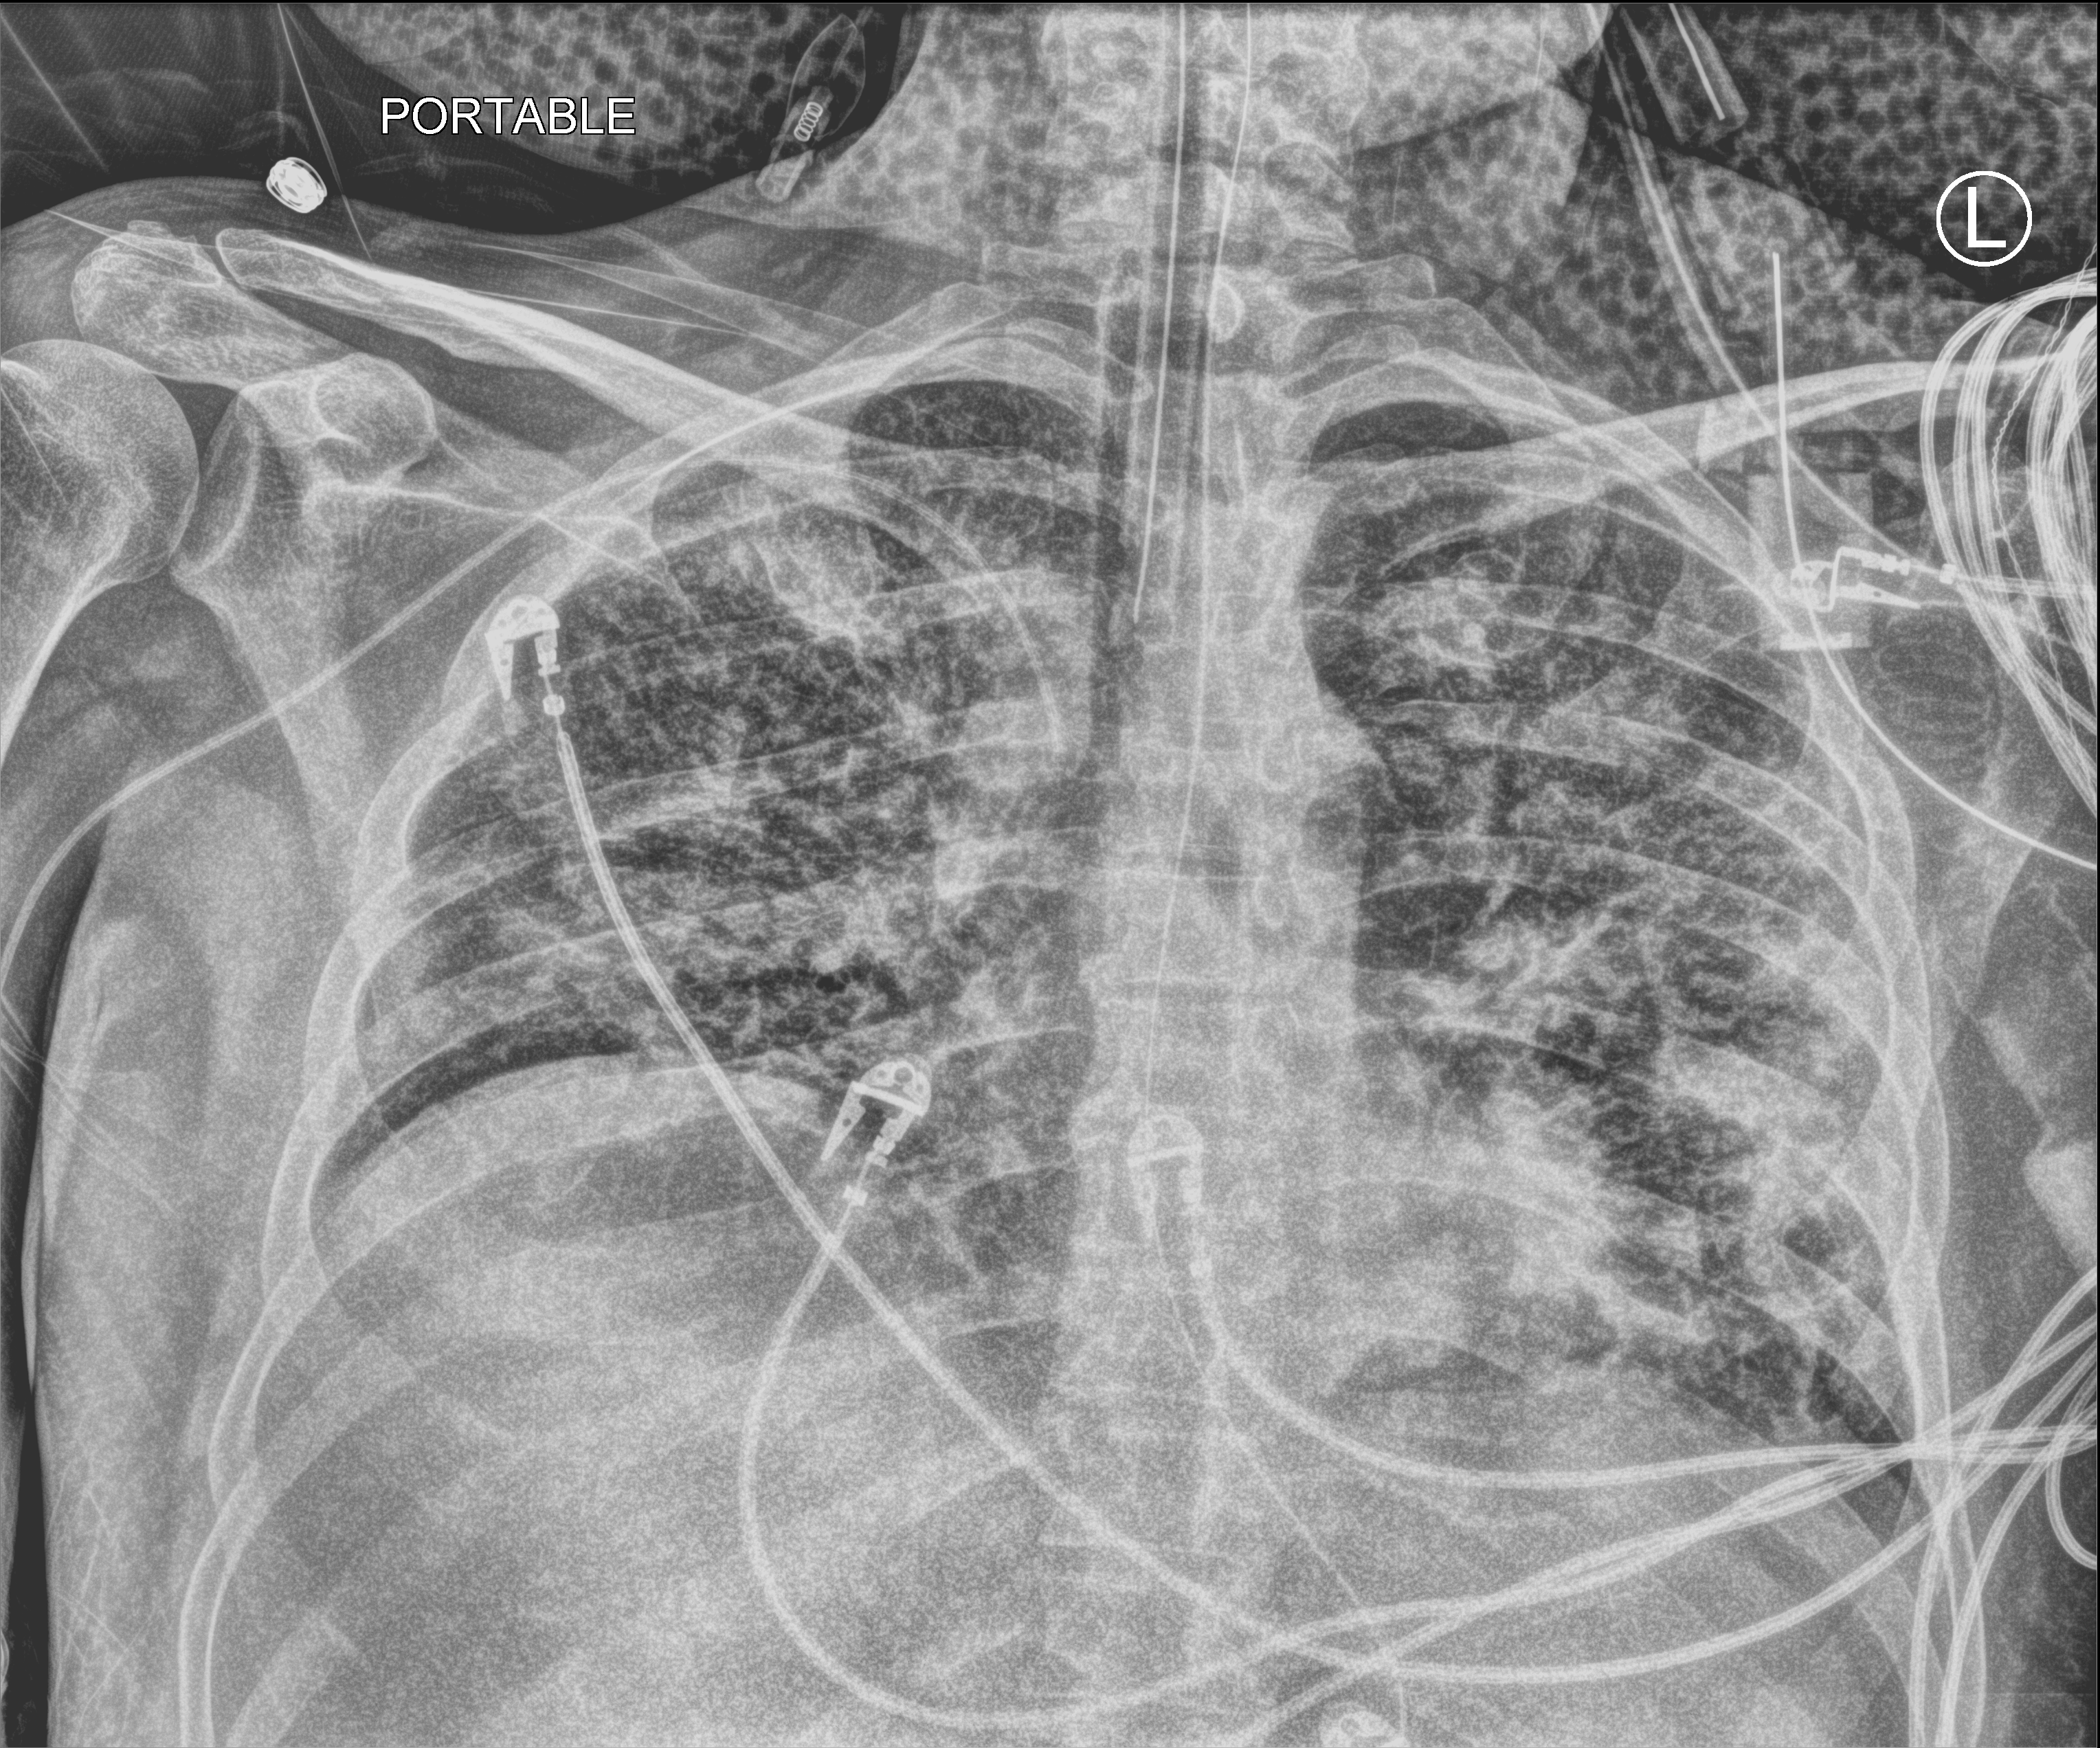
Bedside chest radiograph (computed radiography), anteroposterior (AP) projection. Patient hospitalised with COVID-19; male, aged 18–59 years.
Hospital-stay facts (about this admission, not read from this image; timing relative to this image not recorded):
- other chronic lung disease (admission record): no
- admitted to intensive care during this hospital stay: yes